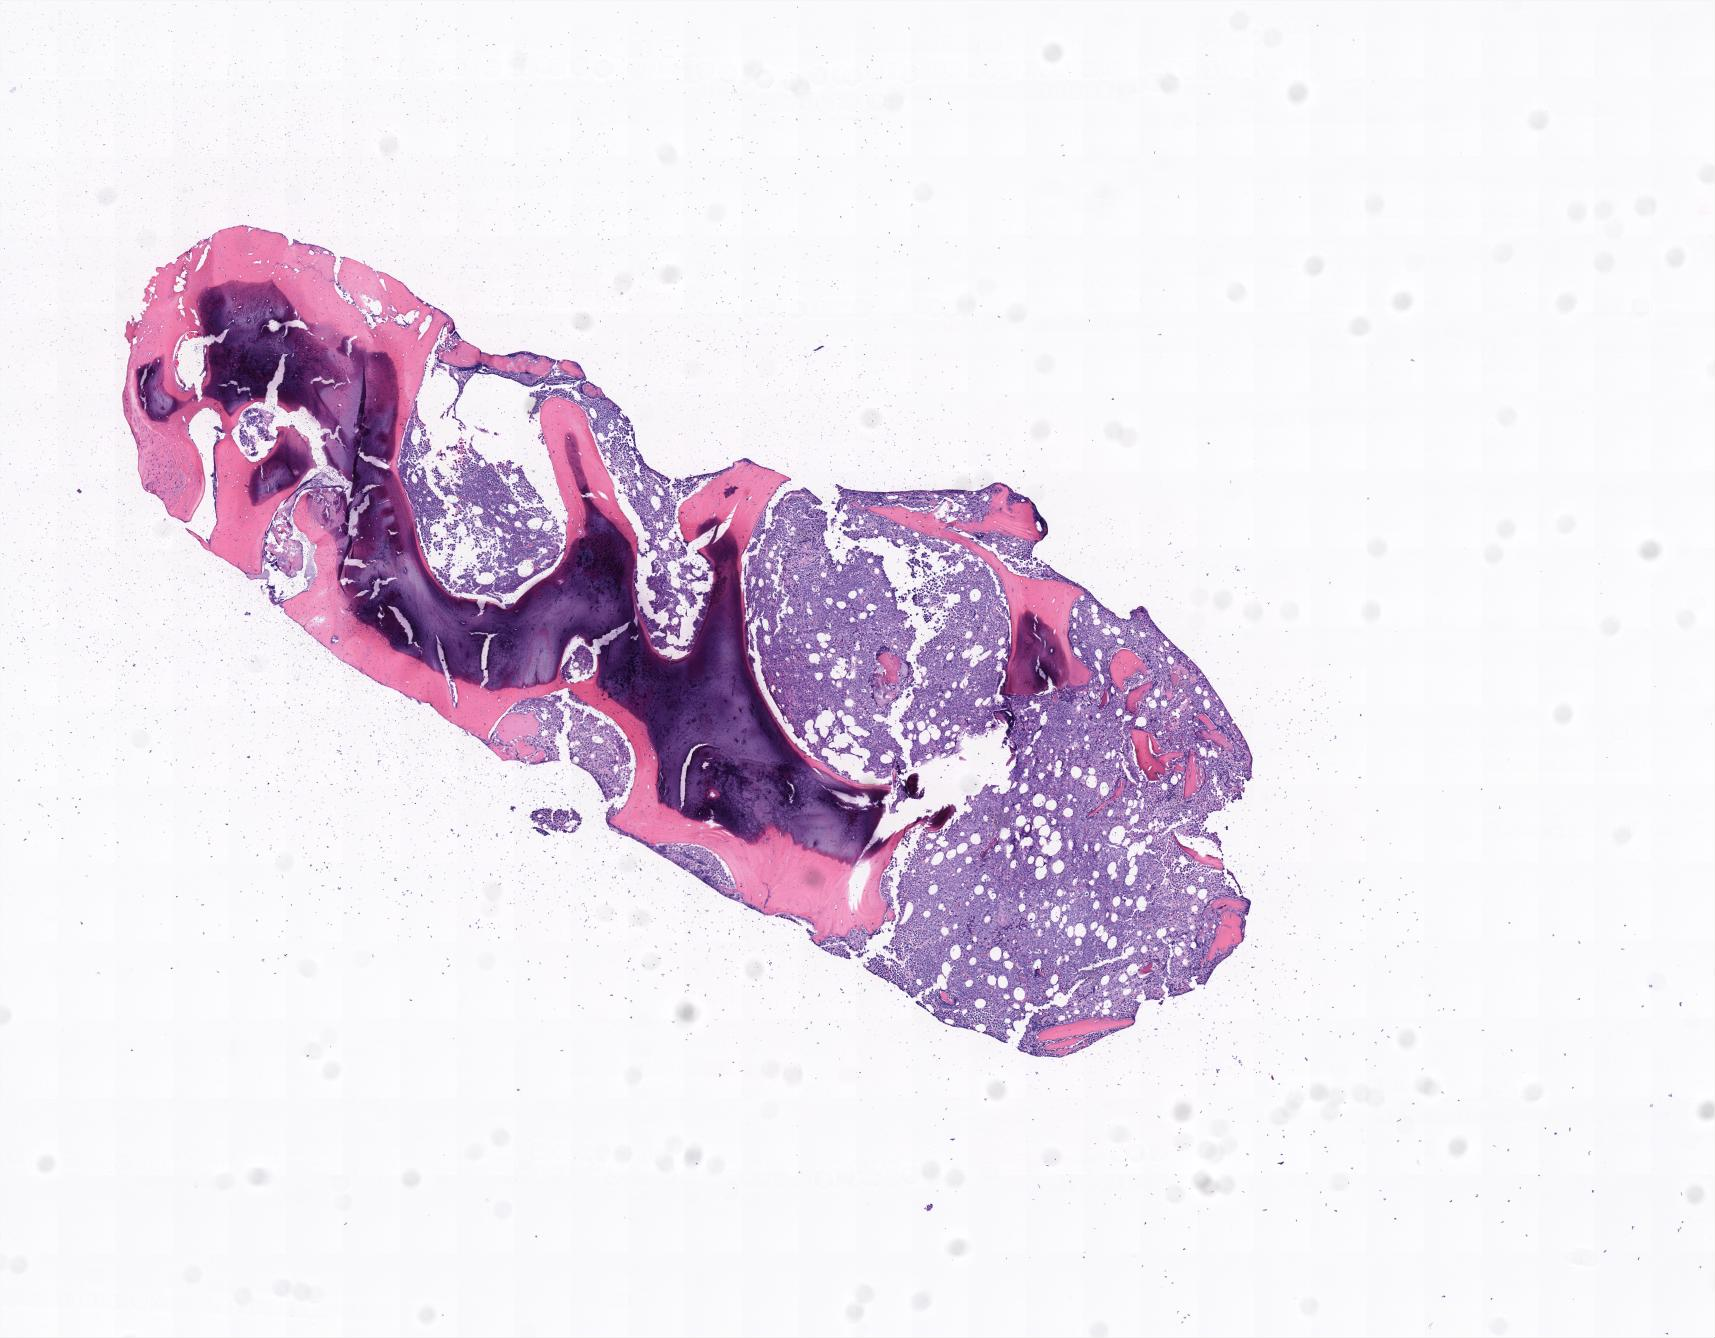
Digitized haematoxylin and eosin-stained section, whole scanned area shown as a low-resolution overview, specimen: tumor tissue, site: bone marrow. Patient: male, 15 years old.
Diagnosis: Burkitt lymphoma, NOS.